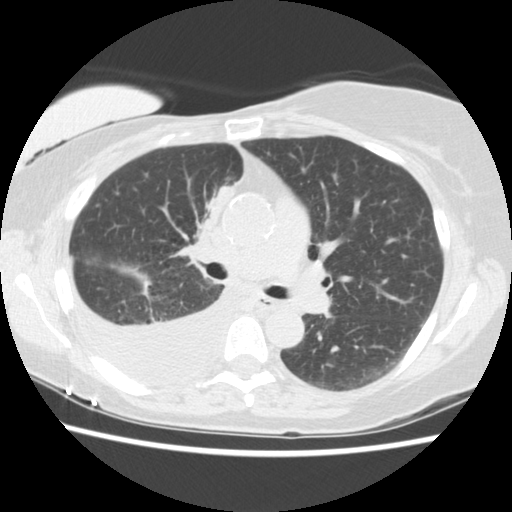
Chest CT (low-dose screening protocol), one axial image; third annual screen; lung window (W 1500 / L -600 HU); 2.5 mm slice thickness; 120 kVp; slice 68 of 157 in the series; 512 × 512 image matrix. Female, age 56 years at enrolment. Current smoker at enrolment.
• Expert-annotated lung lesion, box from (x=184, y=174) to (x=248, y=241) px.
• The screening reader recorded 2 non-calcified nodules or masses ≥4 mm on this exam (right middle lobe, right lower lobe); which of them this box marks is not recorded.
• Official screen result: positive, other.
• Participant outcome: lung cancer diagnosed 160 days after this screen — adenocarcinoma, NOS, right upper lobe, stage IIIB (AJCC 6th edition), 8 mm at pathology.